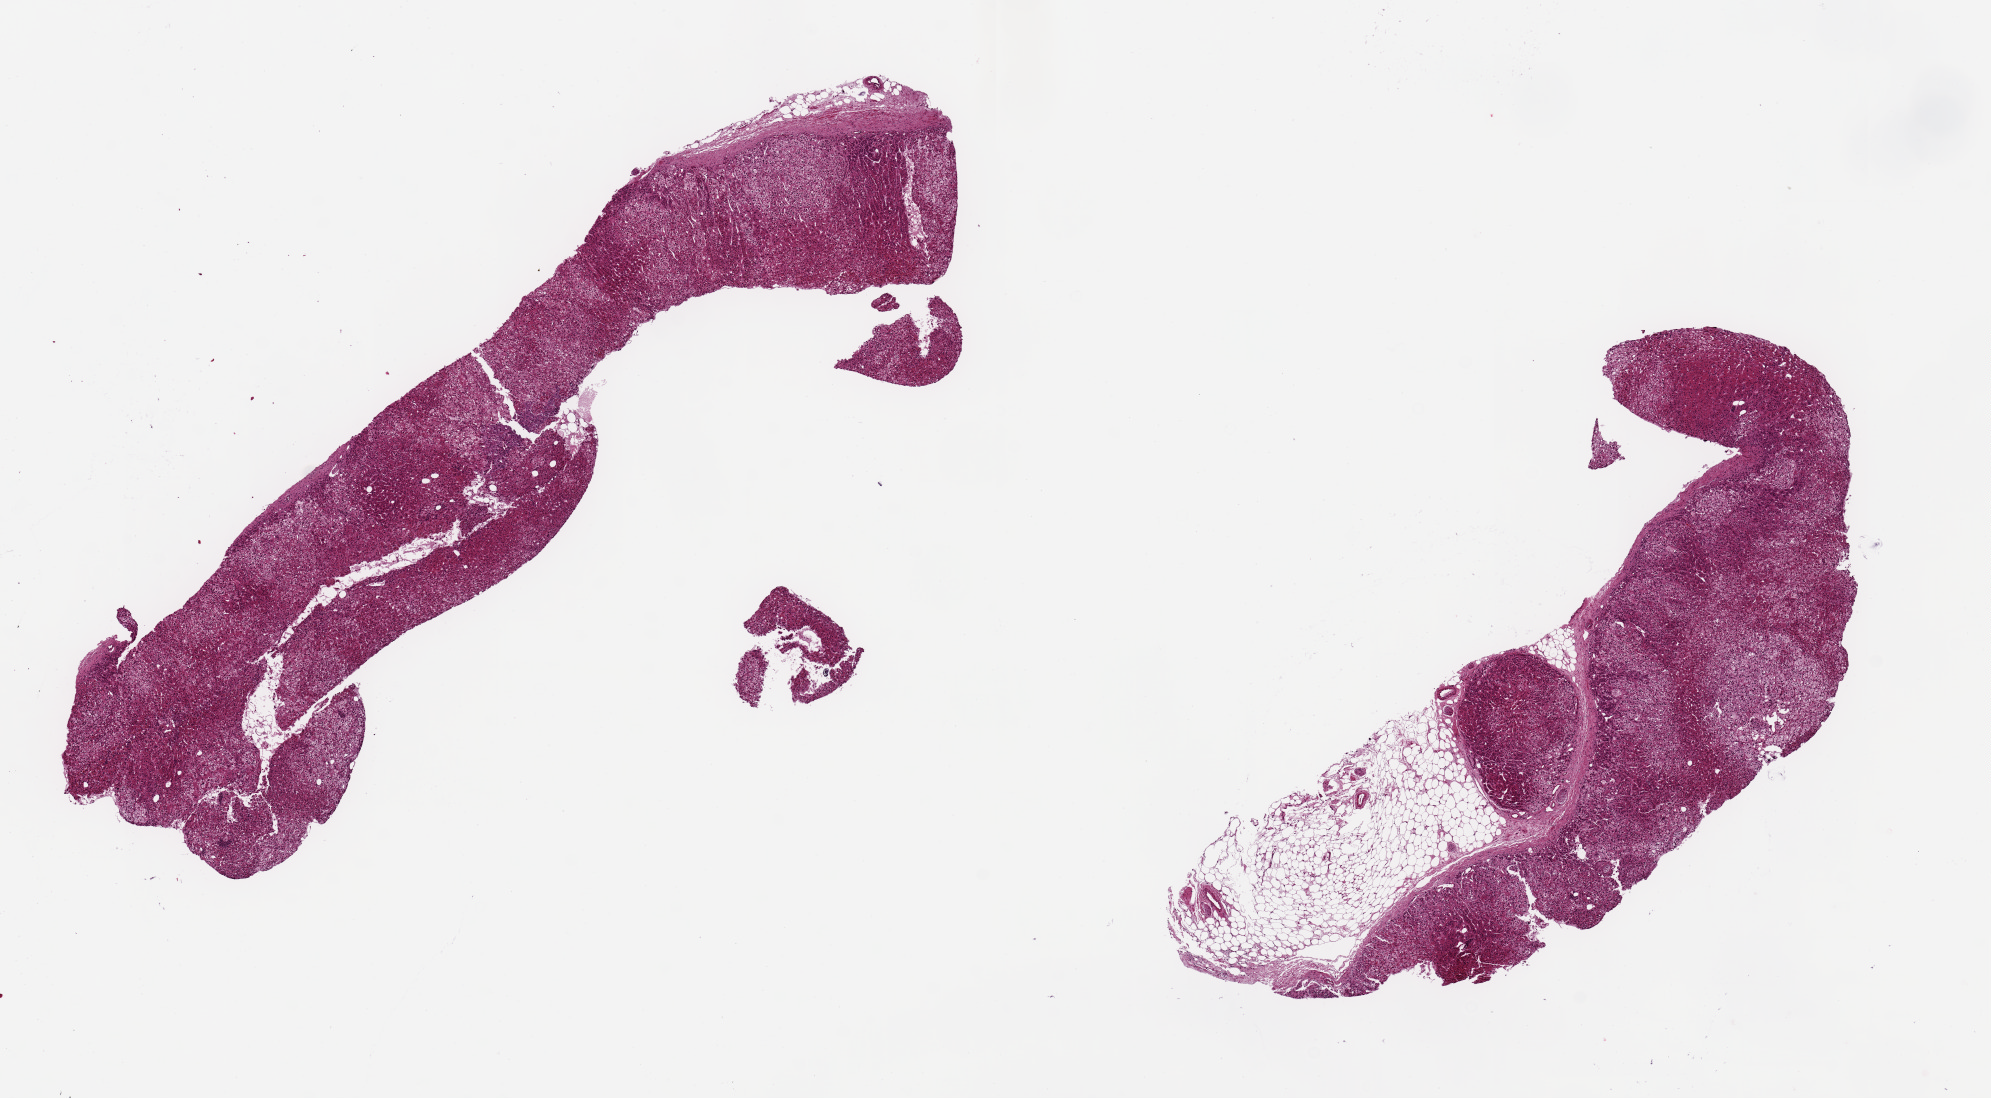
Whole-slide image, hematoxylin and eosin (H&E) stain — low-resolution overview of the scanned area, about 15.8 x 8.7 mm; PAXgene-fixed paraffin-embedded (PFPE) section; section of adrenal gland (target tissue); tissue donor sample. Donor: male.
Reviewer comment on this tissue sample: 2 ~7.5x2mm aliquots, cortex only; one with 2.5x 1.5 mm nodule of fat on one end.